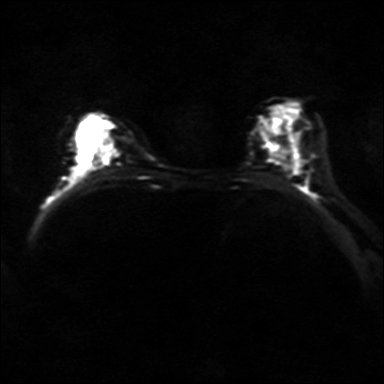
Breast MRI, one axial slice; position 20 of 36 along the scan axis; diffusion-weighted series; image 2 of 4 stored at this slice position (different b-values; order by instance number); 3 T; 4 mm slice thickness; 384 × 384 image matrix, field of view 320 × 320 mm. Female patient.
Annotated regions visible in this slice (expert manual segmentation):
- tumour on diffusion-weighted imaging: box from (x=104, y=146) to (x=120, y=161) px